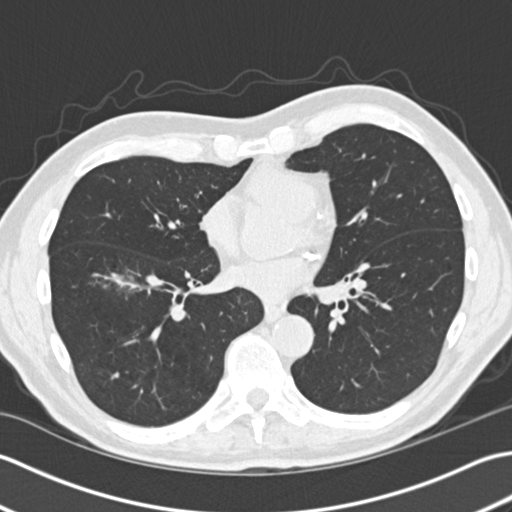
Low-dose screening chest CT, one axial slice. Reconstruction kernel B30f. Lung window (W 1500 / L -600 HU). 2 mm slice thickness. 512 × 512 image matrix.
Outlined on this slice (expert manual segmentation):
- lesion 1 (tumor, lower lobe of right lung): bounding box (x1, y1, x2, y2) in pixels: (93, 273, 142, 291)